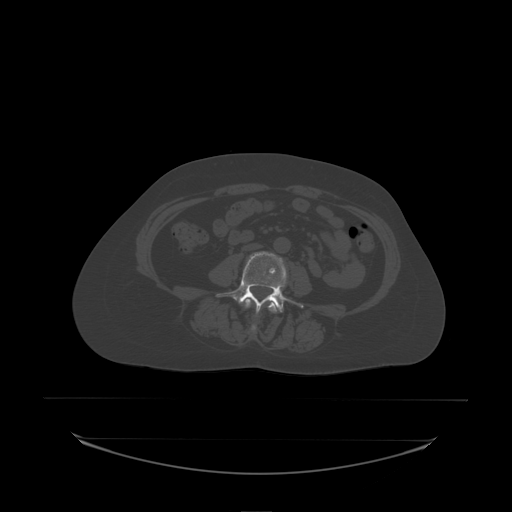
CT including the spine, one axial slice. Position 53 of 242 along the scan axis. Bone window (W 1800 / L 400 HU). 2.5 mm slice thickness. 512 × 512 image matrix. Patient: female, 53 years. Case-level facts recorded for this patient, not image findings: primary cancer: lung.
Annotated regions visible in this slice (semi-automatically segmented with operator editing):
- L3 vertebra: bounding box <245,299,277,330> (left, top, right, bottom; pixels)
- L4 vertebra: <217,251,304,314>